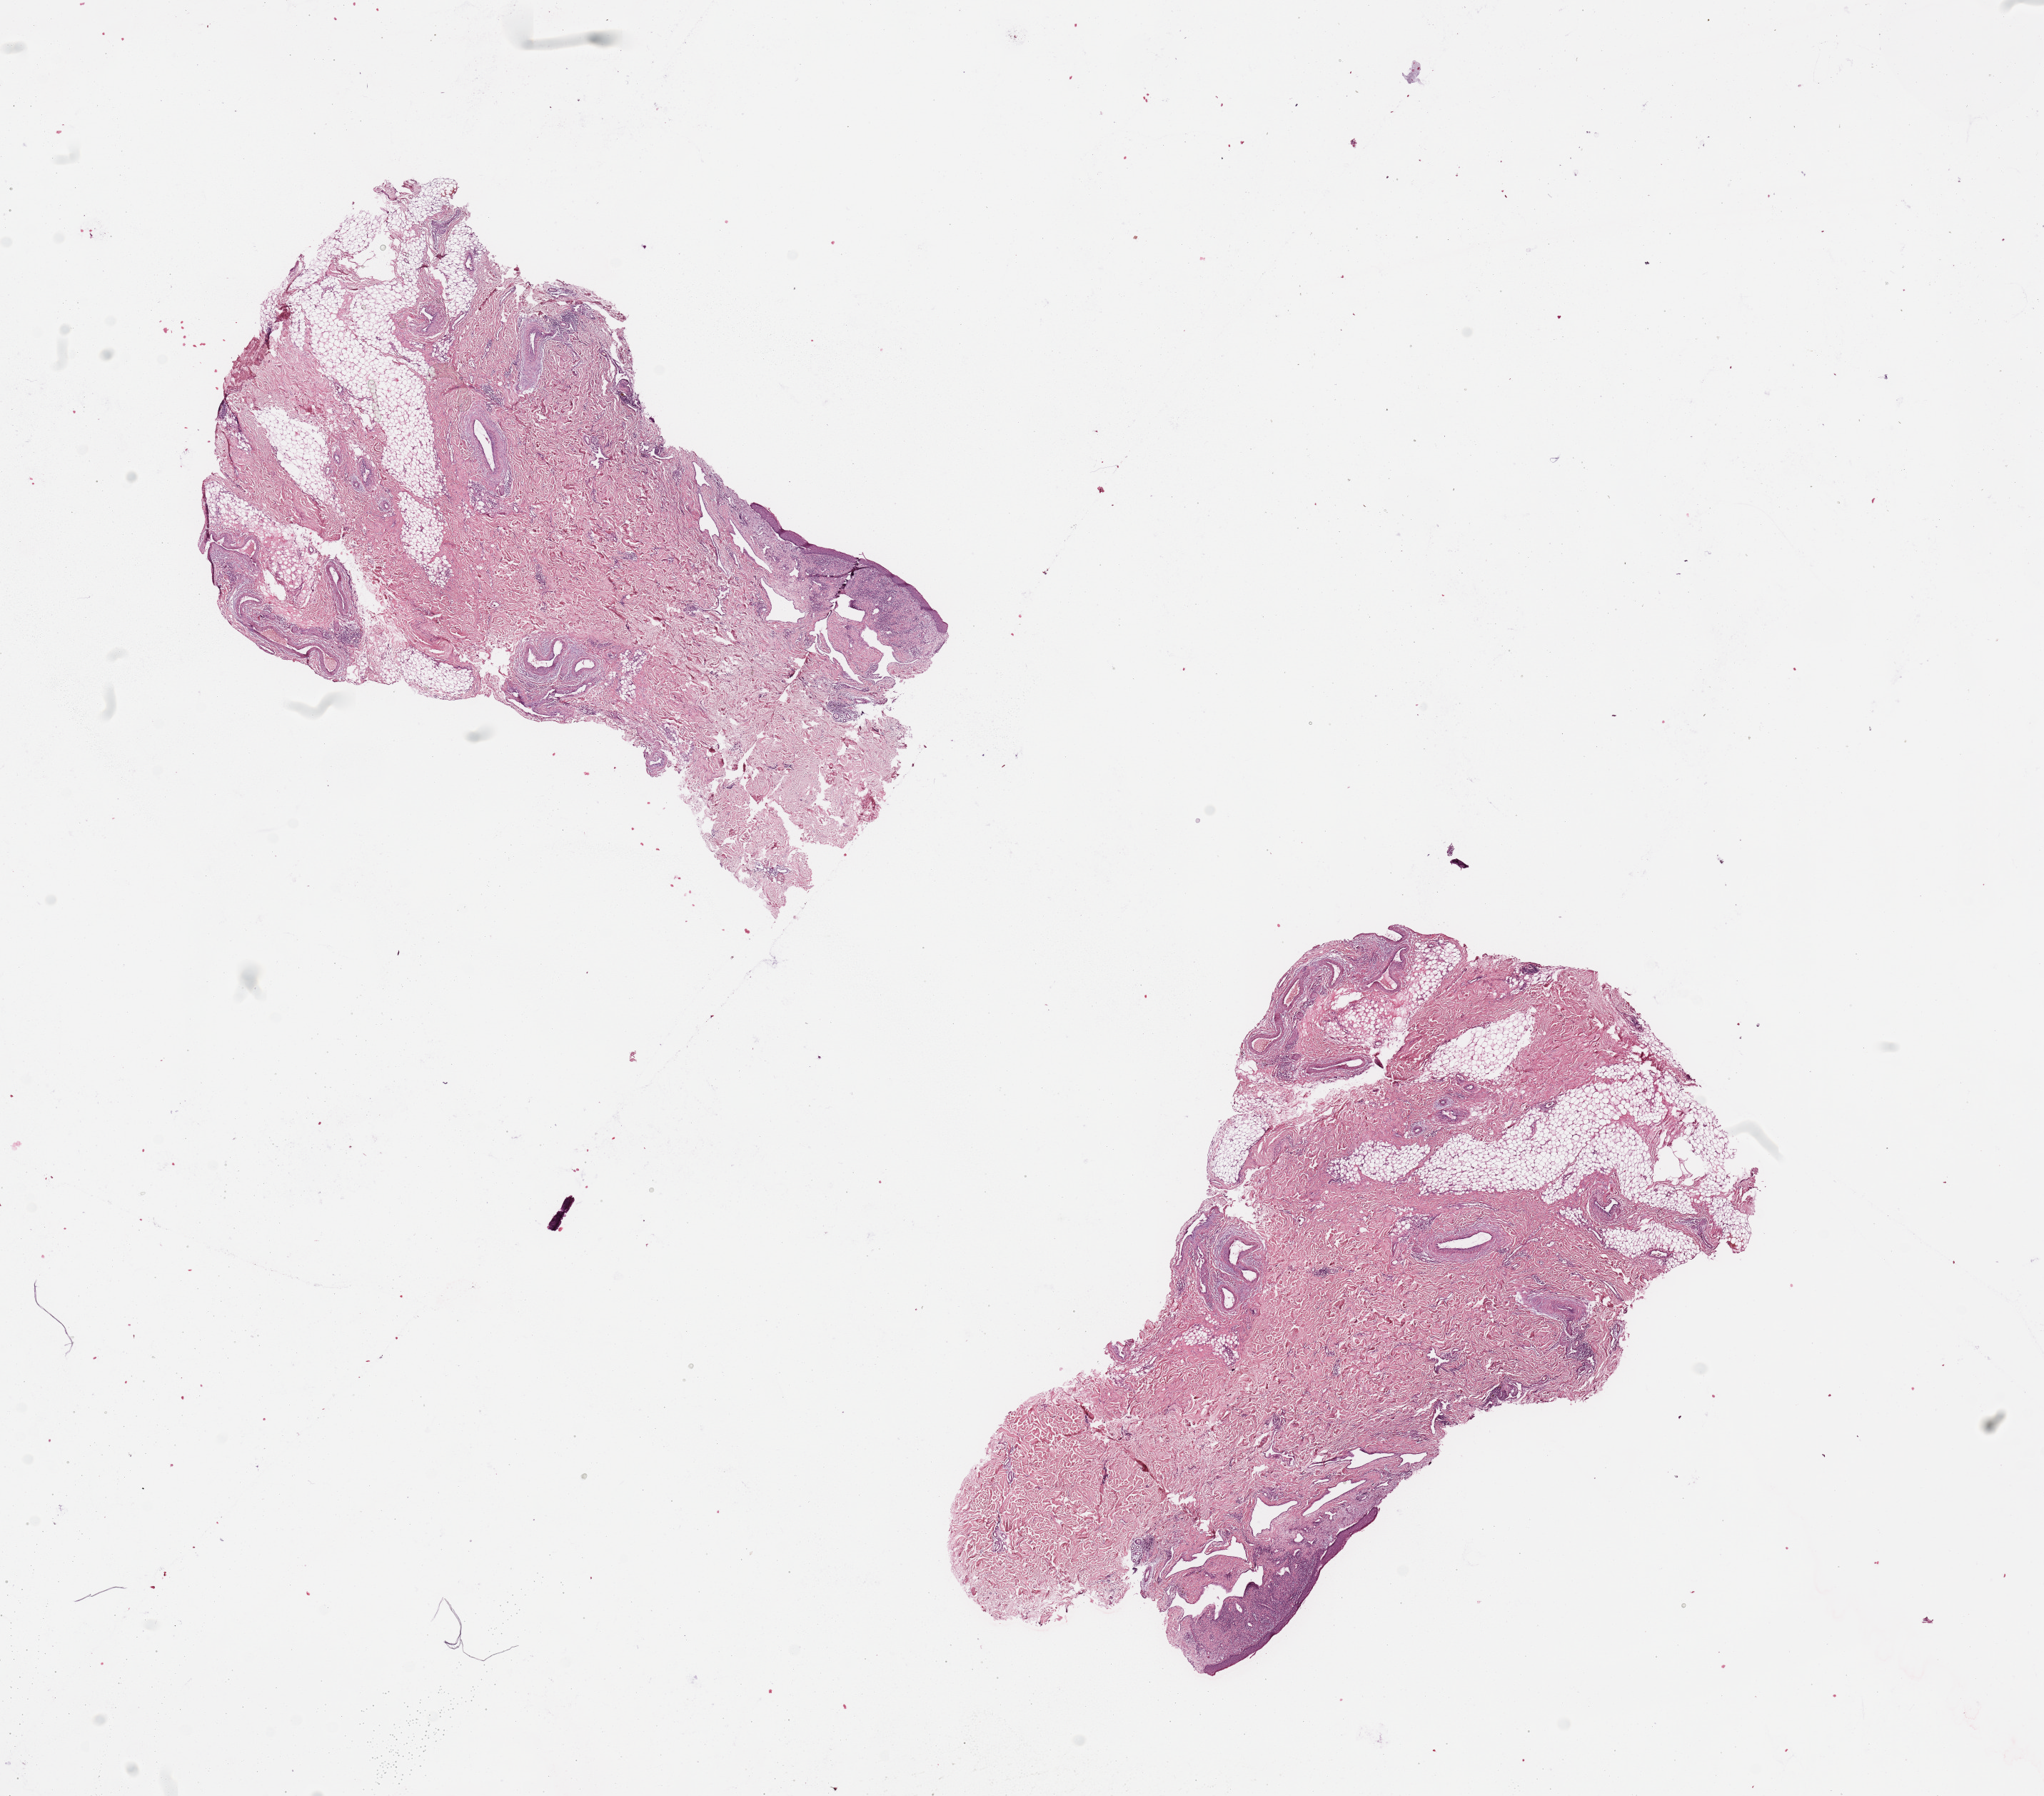
H&E-stained whole-slide image, whole scanned area (about 22.6 x 19.9 mm, from a 20x scan) shown as a low-resolution overview; normal (non-tumour) tissue (melanoma cohort); sampled site not recorded. Male, 75 y/o.
This section: normal (non-tumour) tissue from the same patient. Patient diagnosis: Malignant melanoma, NOS.